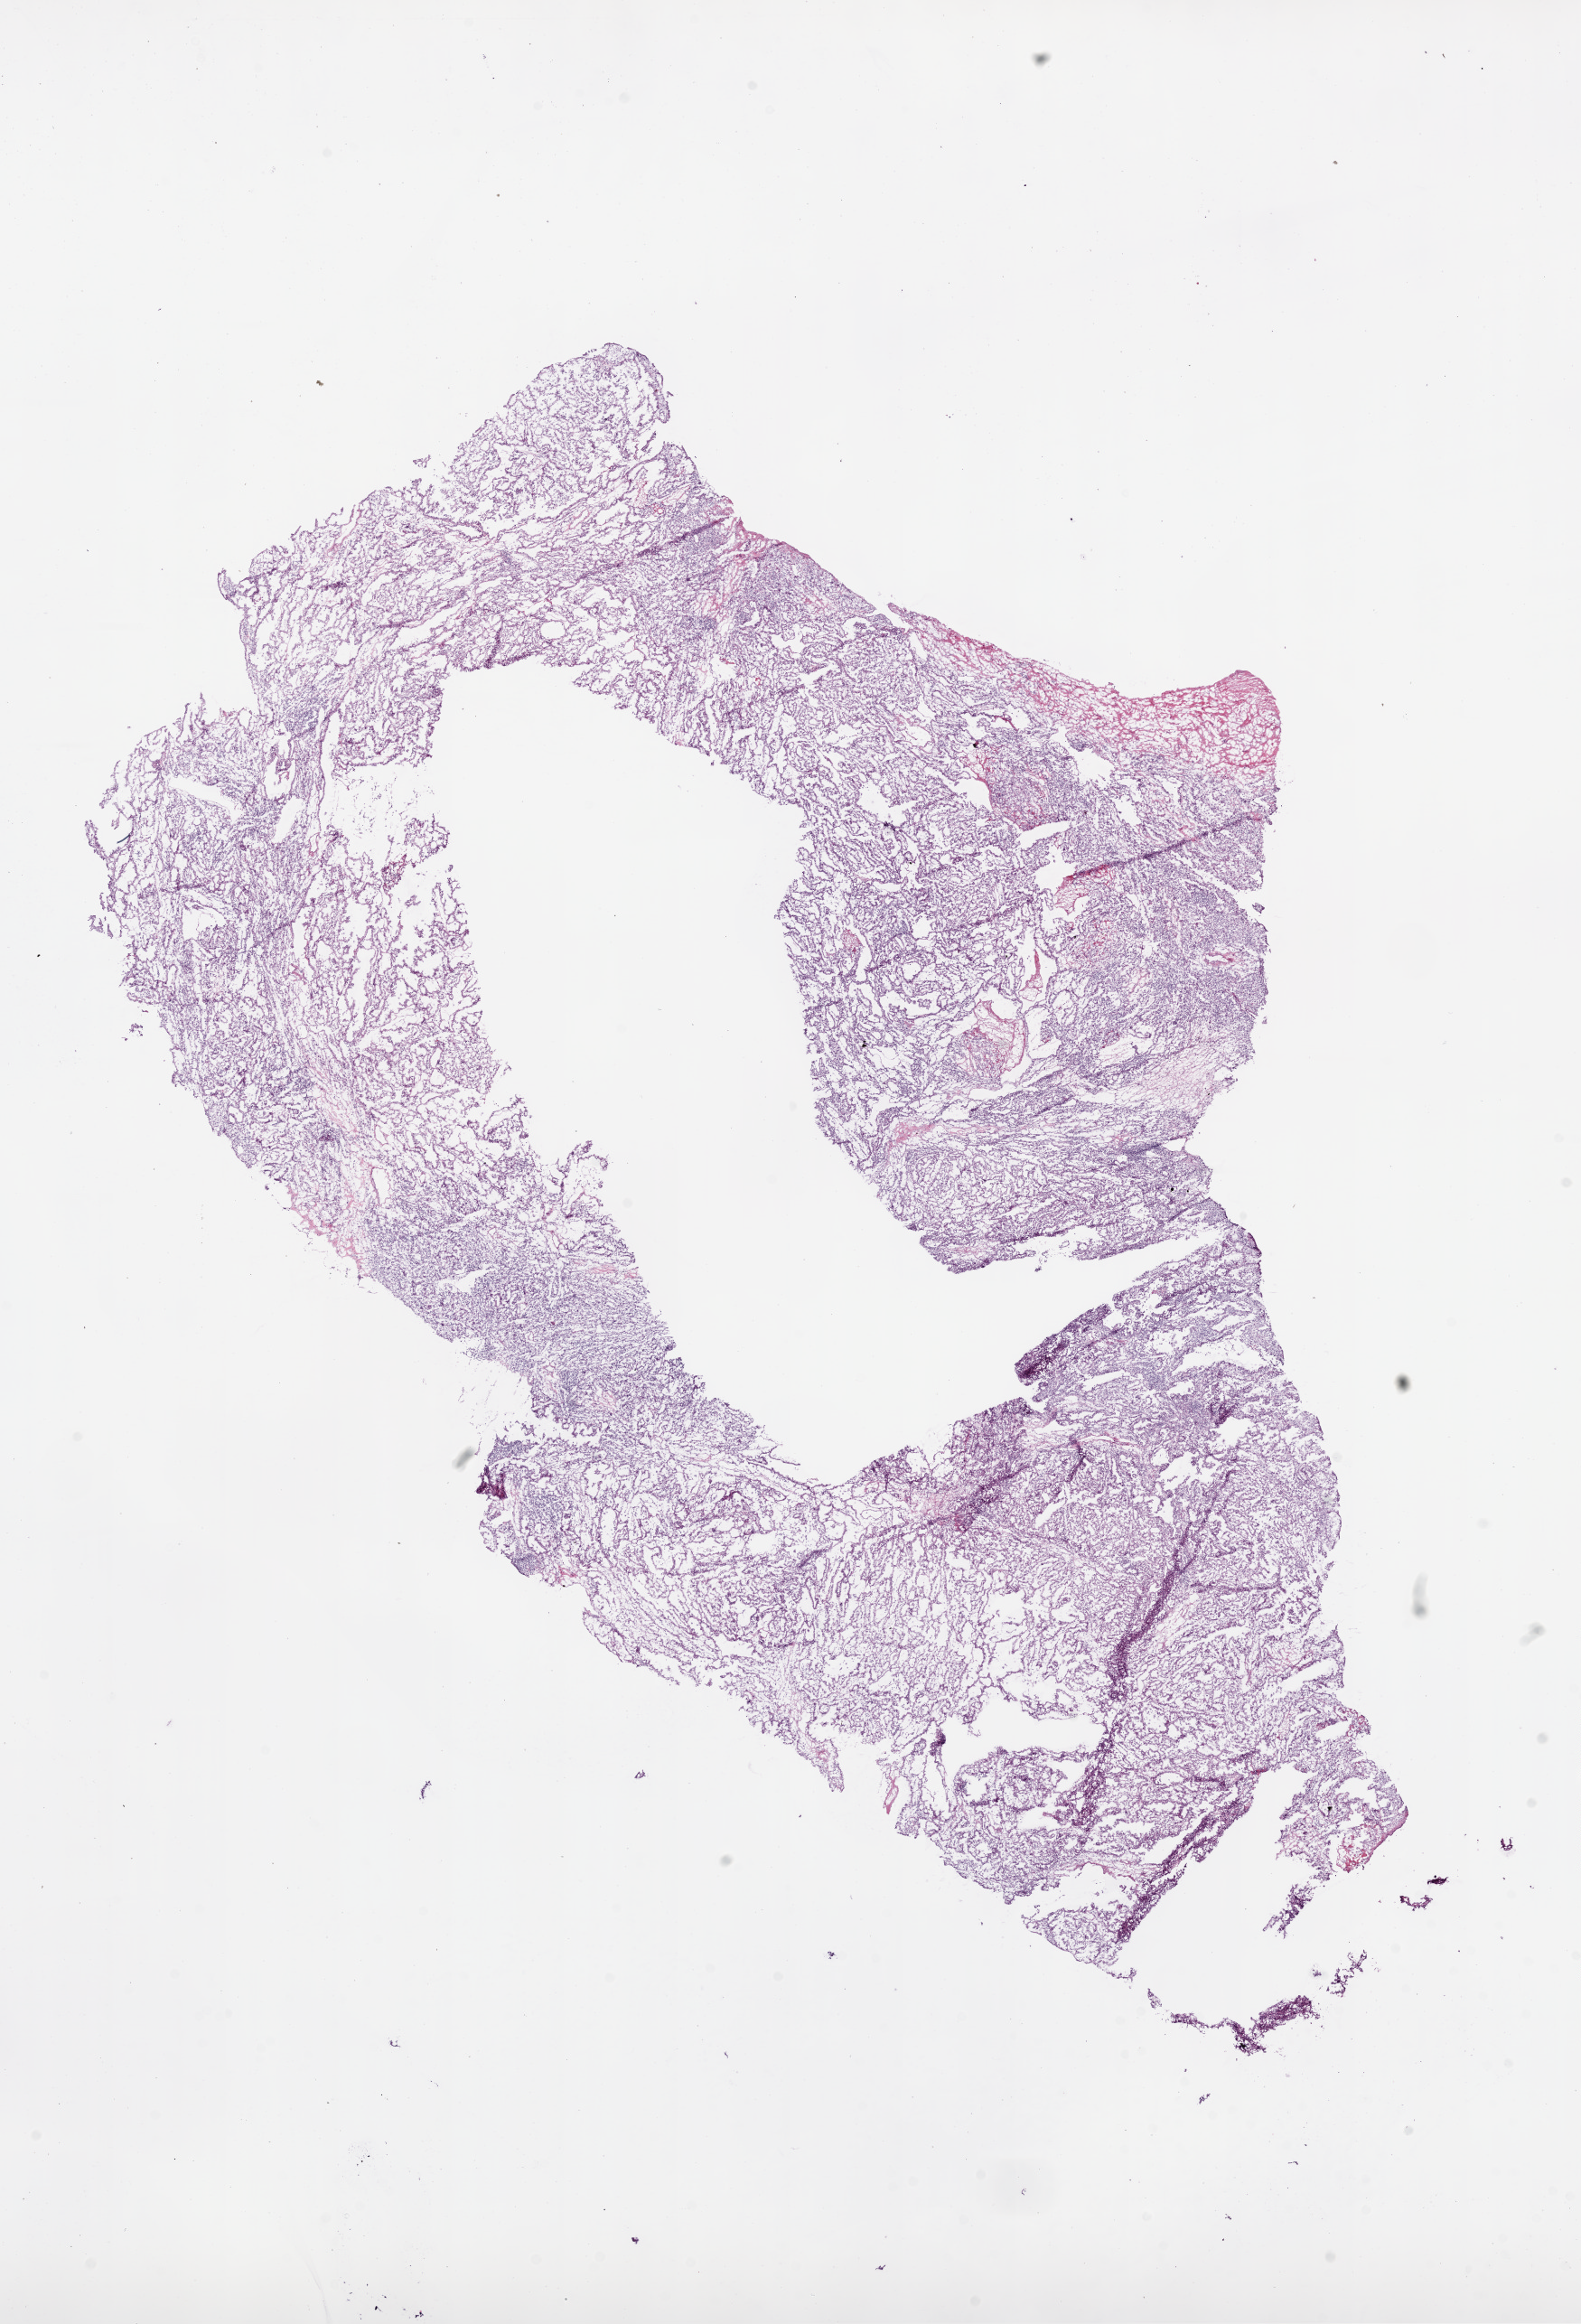
Digitized Hematoxylin and eosin (H&E) stained tissue section (whole slide) — whole scanned area (about 14.0 x 20.6 mm) shown as a low-resolution overview; frozen section from the bottom of the tissue portion; primary tumour sample from the kidney. Male patient; age at initial diagnosis 46 years. Histologic grade: G2 (moderately differentiated). Slide review estimates, as recorded: tumour cells 90%, tumour nuclei 80%, normal cells 0%, stromal cells 10%, necrosis 0%.
TNM: T1b NX M0. Laterality: left. Pathologic diagnosis: Clear cell adenocarcinoma, NOS. AJCC pathologic stage: I.